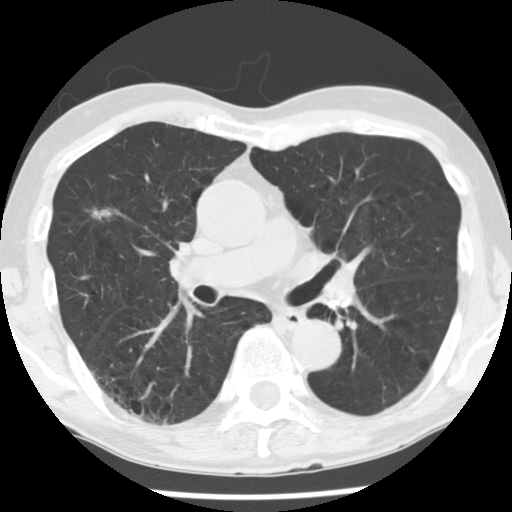
Chest CT (low-dose screening protocol), one axial image; baseline screening round; lung window (W 1500 / L -600 HU); 2.5 mm slice thickness; standard (soft-tissue) reconstruction kernel (STANDARD); 120 kVp; slice 79 of 176 in the series. Male participant, aged 72 years at enrolment.
Lesion marked by an expert reader, bounding box [x1, y1, x2, y2] px = [76, 197, 133, 237]. Reader record for this screening exam (exam-level; its link to the box is not recorded): non-calcified nodule or mass ≥4 mm, right upper lobe, 11 × 8 mm, spiculated (stellate) margins, soft tissue attenuation. Official screen result: positive, change unspecified: nodule(s) >= 4 mm or enlarging nodule(s), mass(es), or other non-specific abnormalities suspicious for lung cancer. Participant outcome: lung cancer diagnosed 72 days after this screen — bronchiolo-alveolar adenocarcinoma, NOS, right upper lobe, moderately differentiated (G2), stage IA (AJCC 6th edition), 10 mm at pathology.